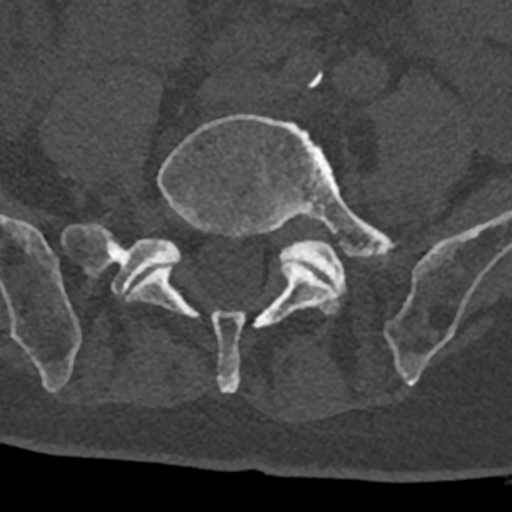
CT including the spine, one axial slice; position 189 of 797 along the scan axis; reconstruction kernel Br40s/3; bone window (W 1800 / L 400 HU); 0.5 mm slice thickness; 512 × 512 image matrix, field of view 160 × 160 mm. Male patient, age 74 years. From the clinical record (not read from this slice): primary cancer: renal.
Annotated regions visible in this slice (semi-automatic segmentation, software-assisted and operator-edited):
- L4 vertebra: box from (x=319, y=72) to (x=322, y=74) px
- L5 vertebra: (x=127, y=114)–(x=396, y=394)